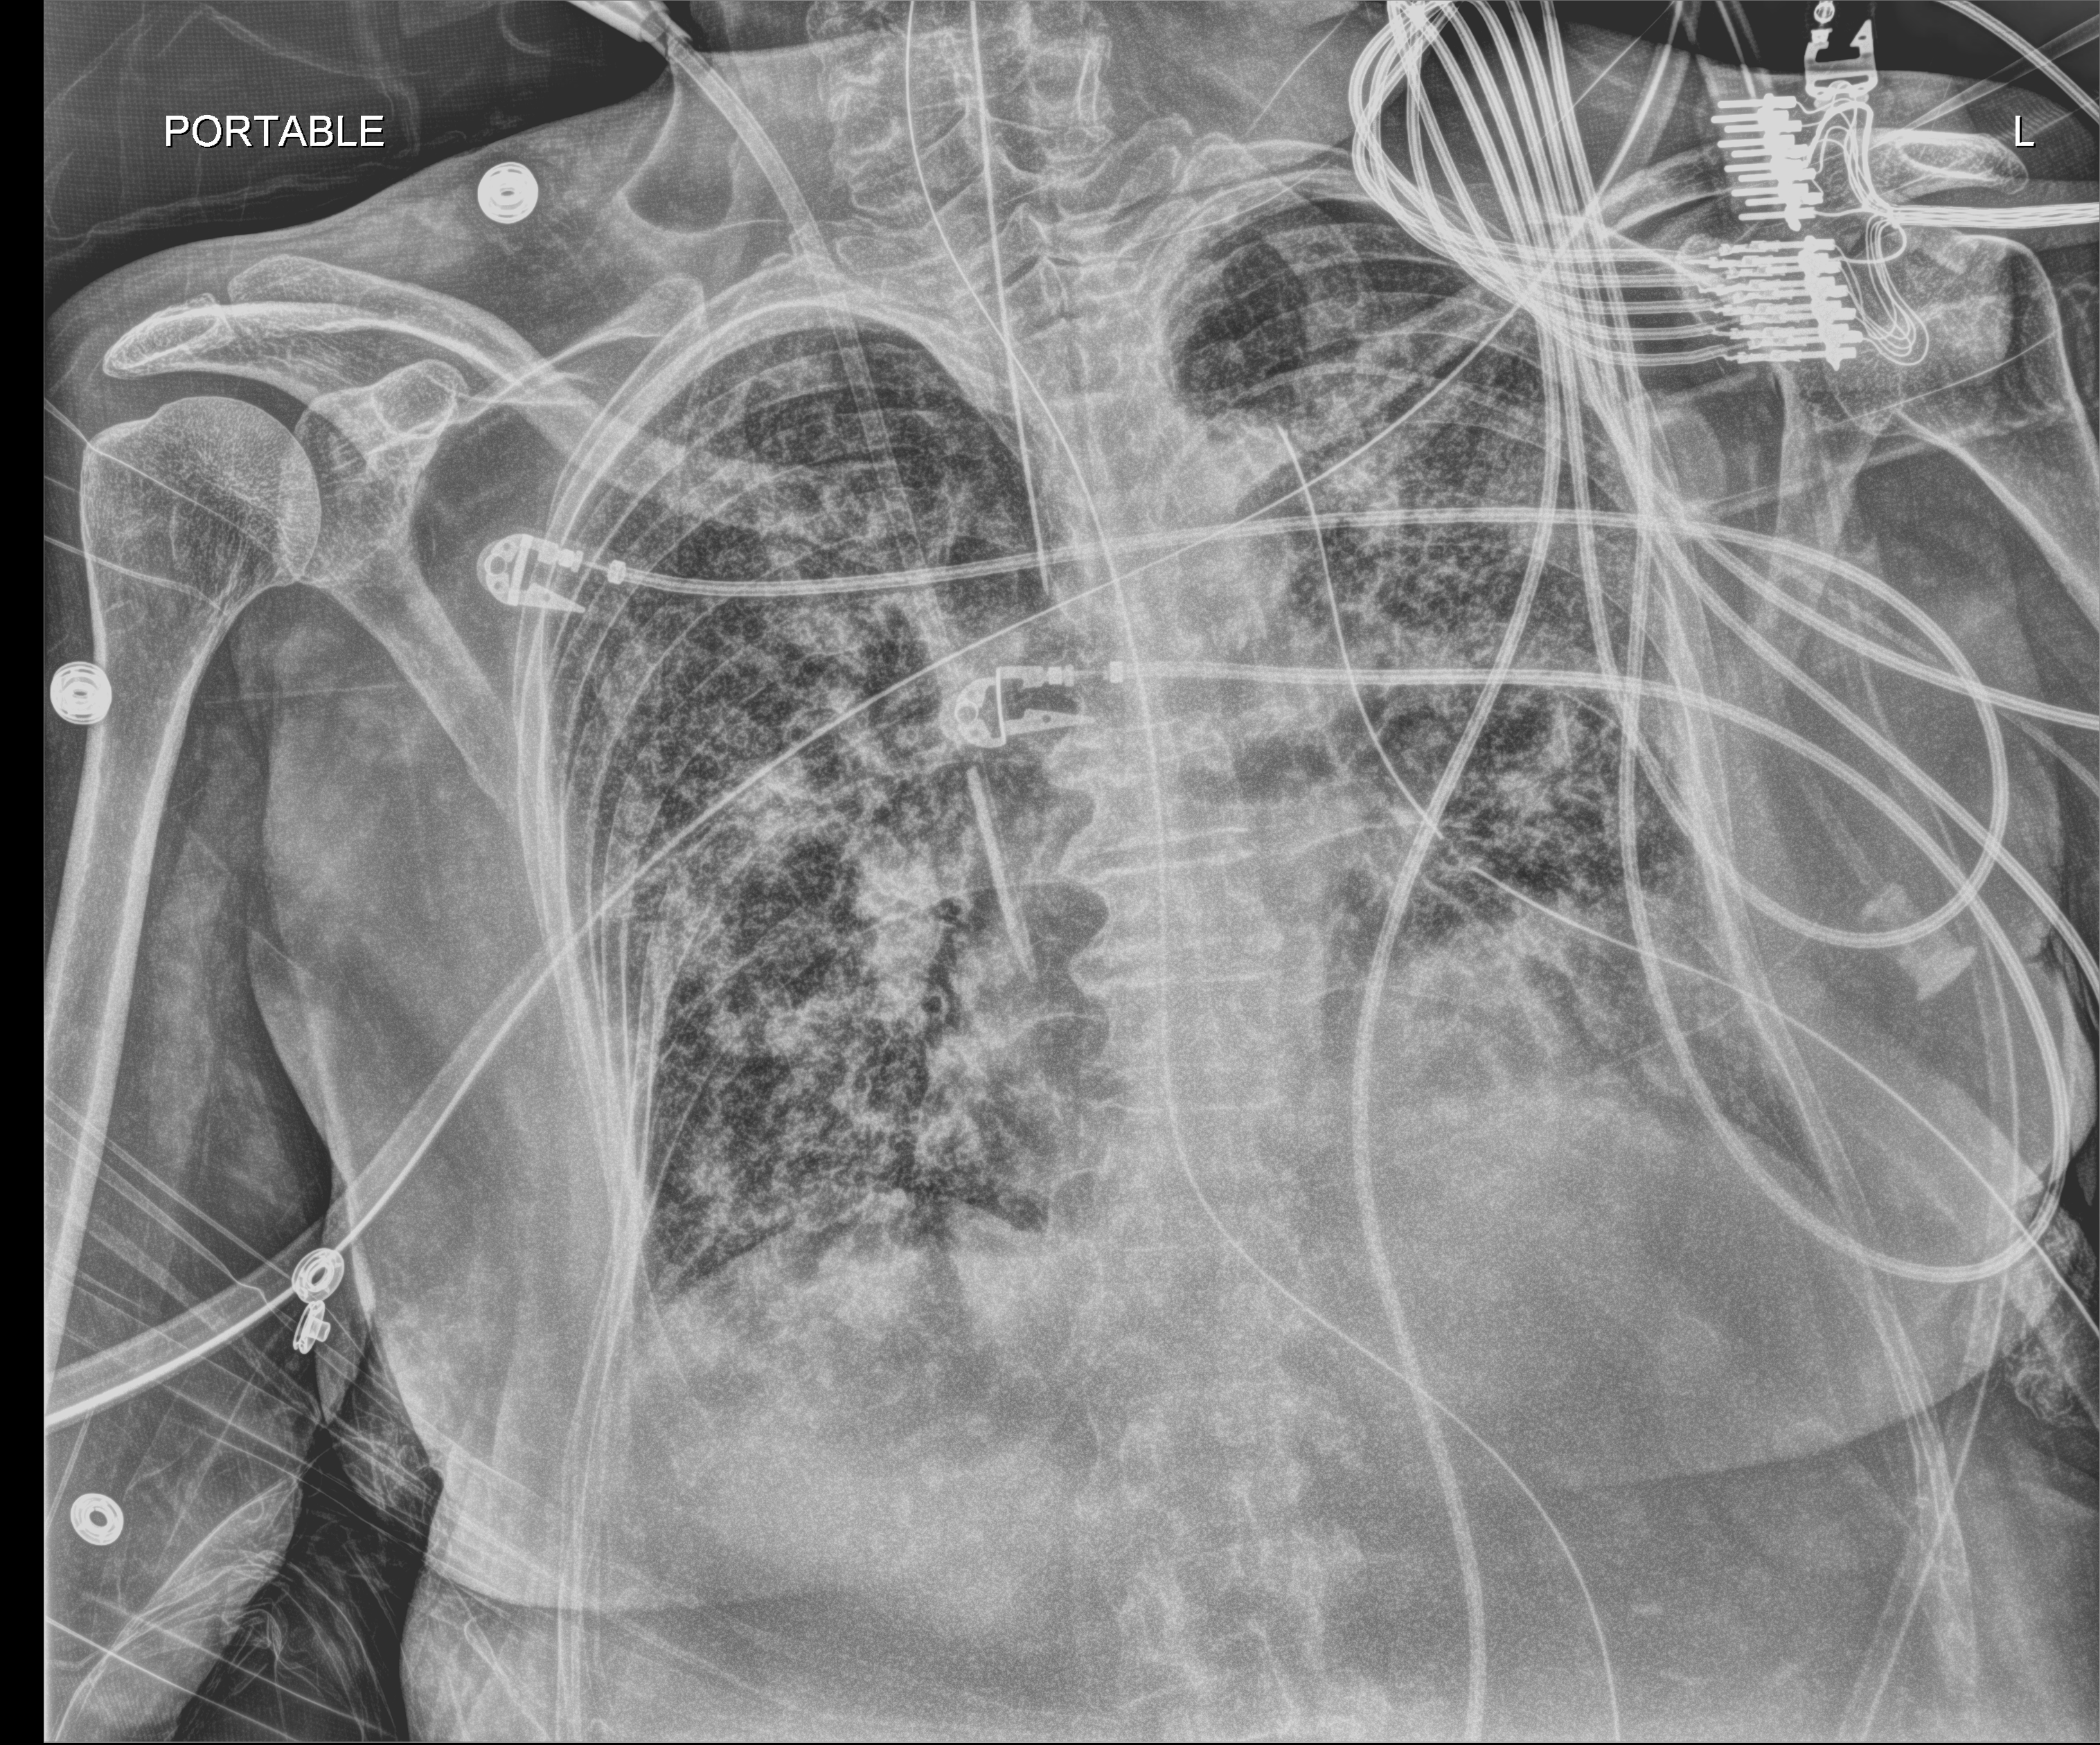
Chest X-ray (portable); anteroposterior (AP) projection. Patient hospitalised with COVID-19; female, aged 75–90 years.
Admission-level facts for this patient (not findings on this image; timing relative to this image not recorded):
- mechanically ventilated during this hospital stay: yes
- admitted to intensive care during this hospital stay: yes
- length of hospital stay: 70 days